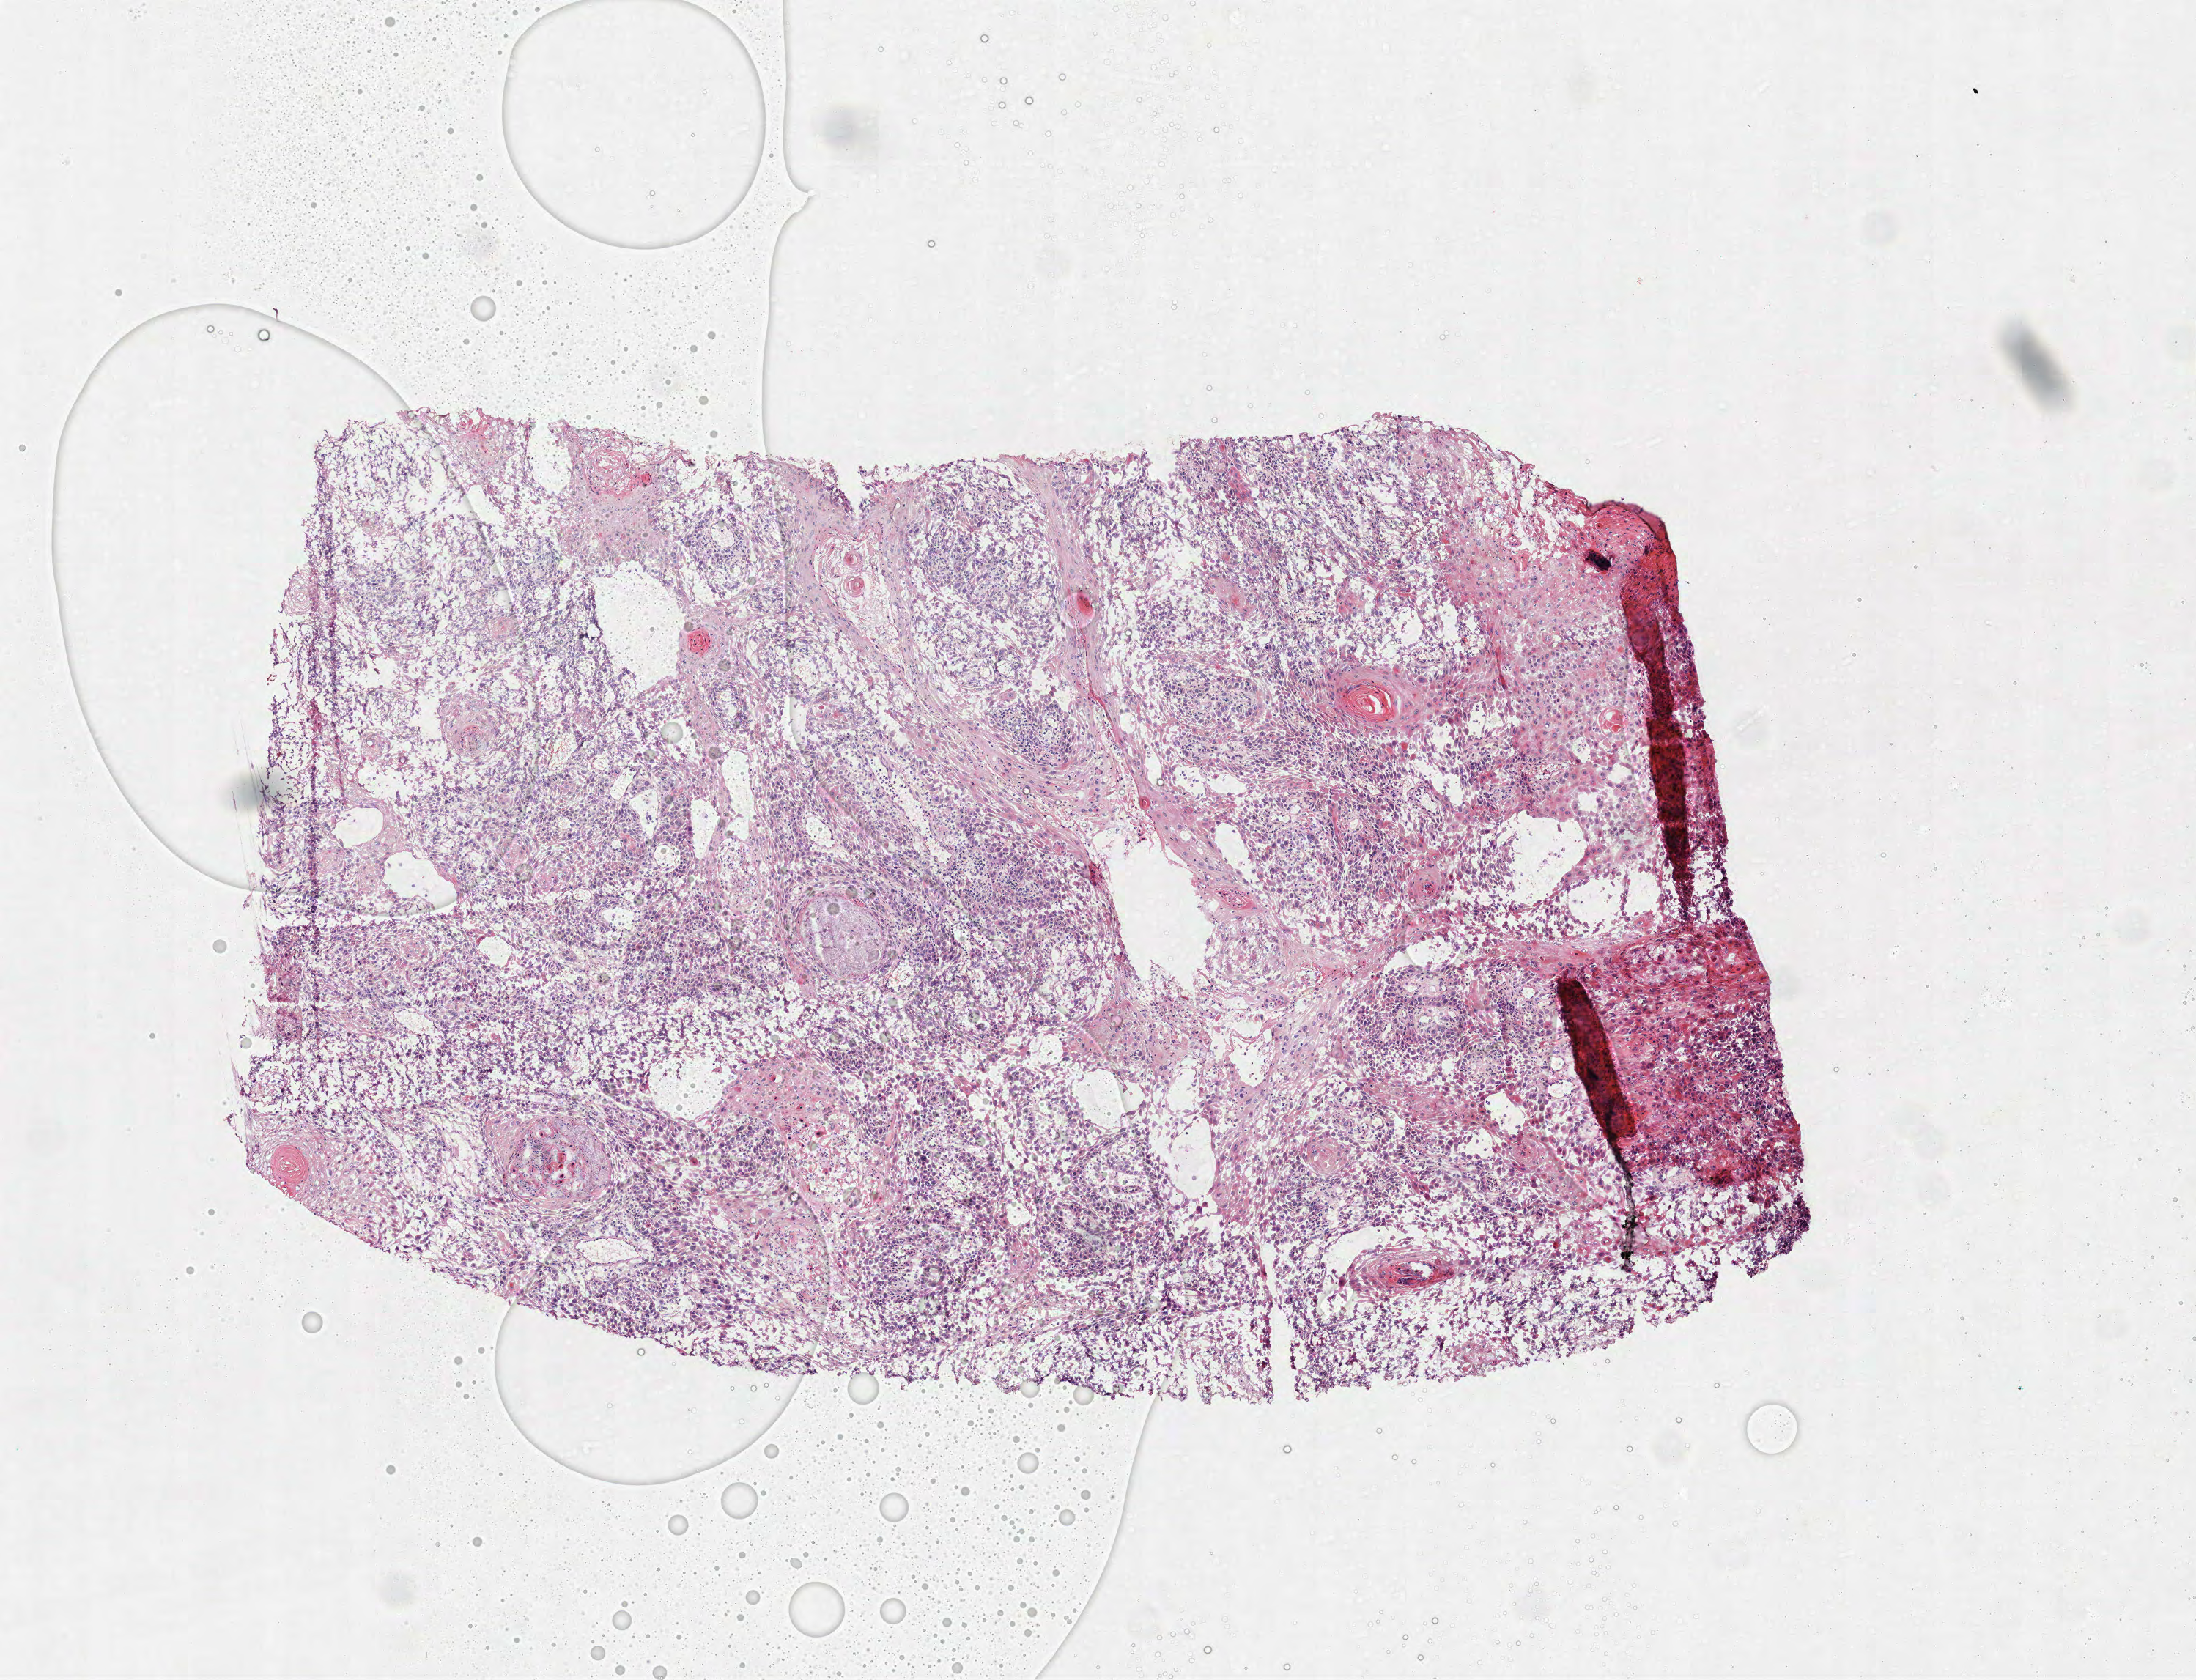
Digitized H&E-stained tissue section (whole slide), whole scanned area (about 6.0 x 4.6 mm) shown as a low-resolution overview; frozen section from the top of the tissue portion; primary tumour sample from the head and neck. Patient: male, age at initial diagnosis 69 years. Histologic grade: G2 (moderately differentiated). Pathologist review of this section (percent, as recorded): tumour cells 90%, tumour nuclei 80%, normal cells 0%, stromal cells 10%, necrosis 0%.
Lymph nodes positive (case pathology): 0 of 8 examined. AJCC pathologic stage: I (7th edition). Laterality: right. Diagnosis: Squamous cell carcinoma, NOS (lip, NOS).